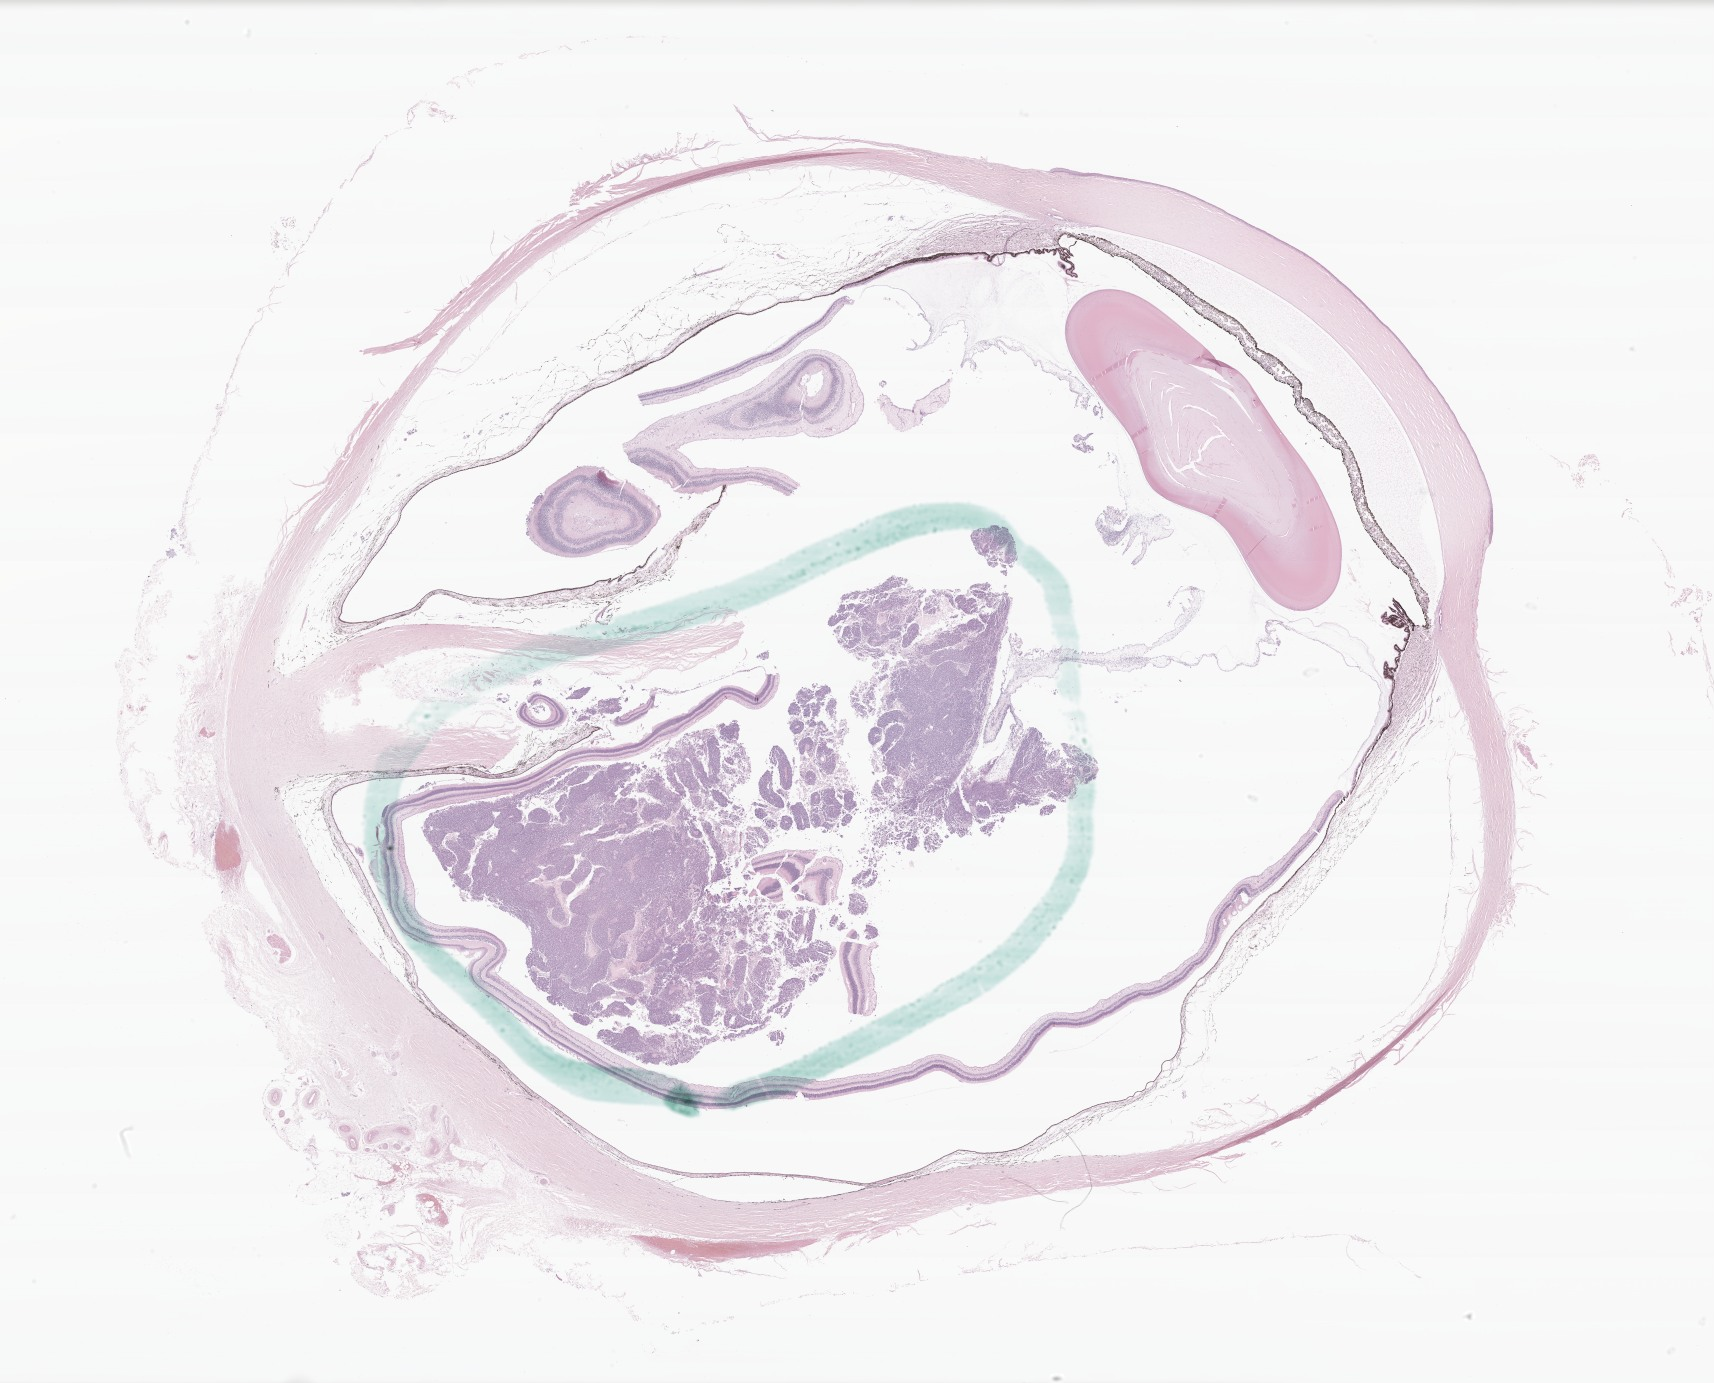
Whole-slide image, haematoxylin and eosin stain of tumor tissue from the retina, a low-resolution overview of the entire scanned area, about 28.8 x 23.3 mm; formalin-fixed paraffin-embedded section. Patient: female, age 416 days (about 1.1 years).
• diagnosis: Retinoblastoma, NOS